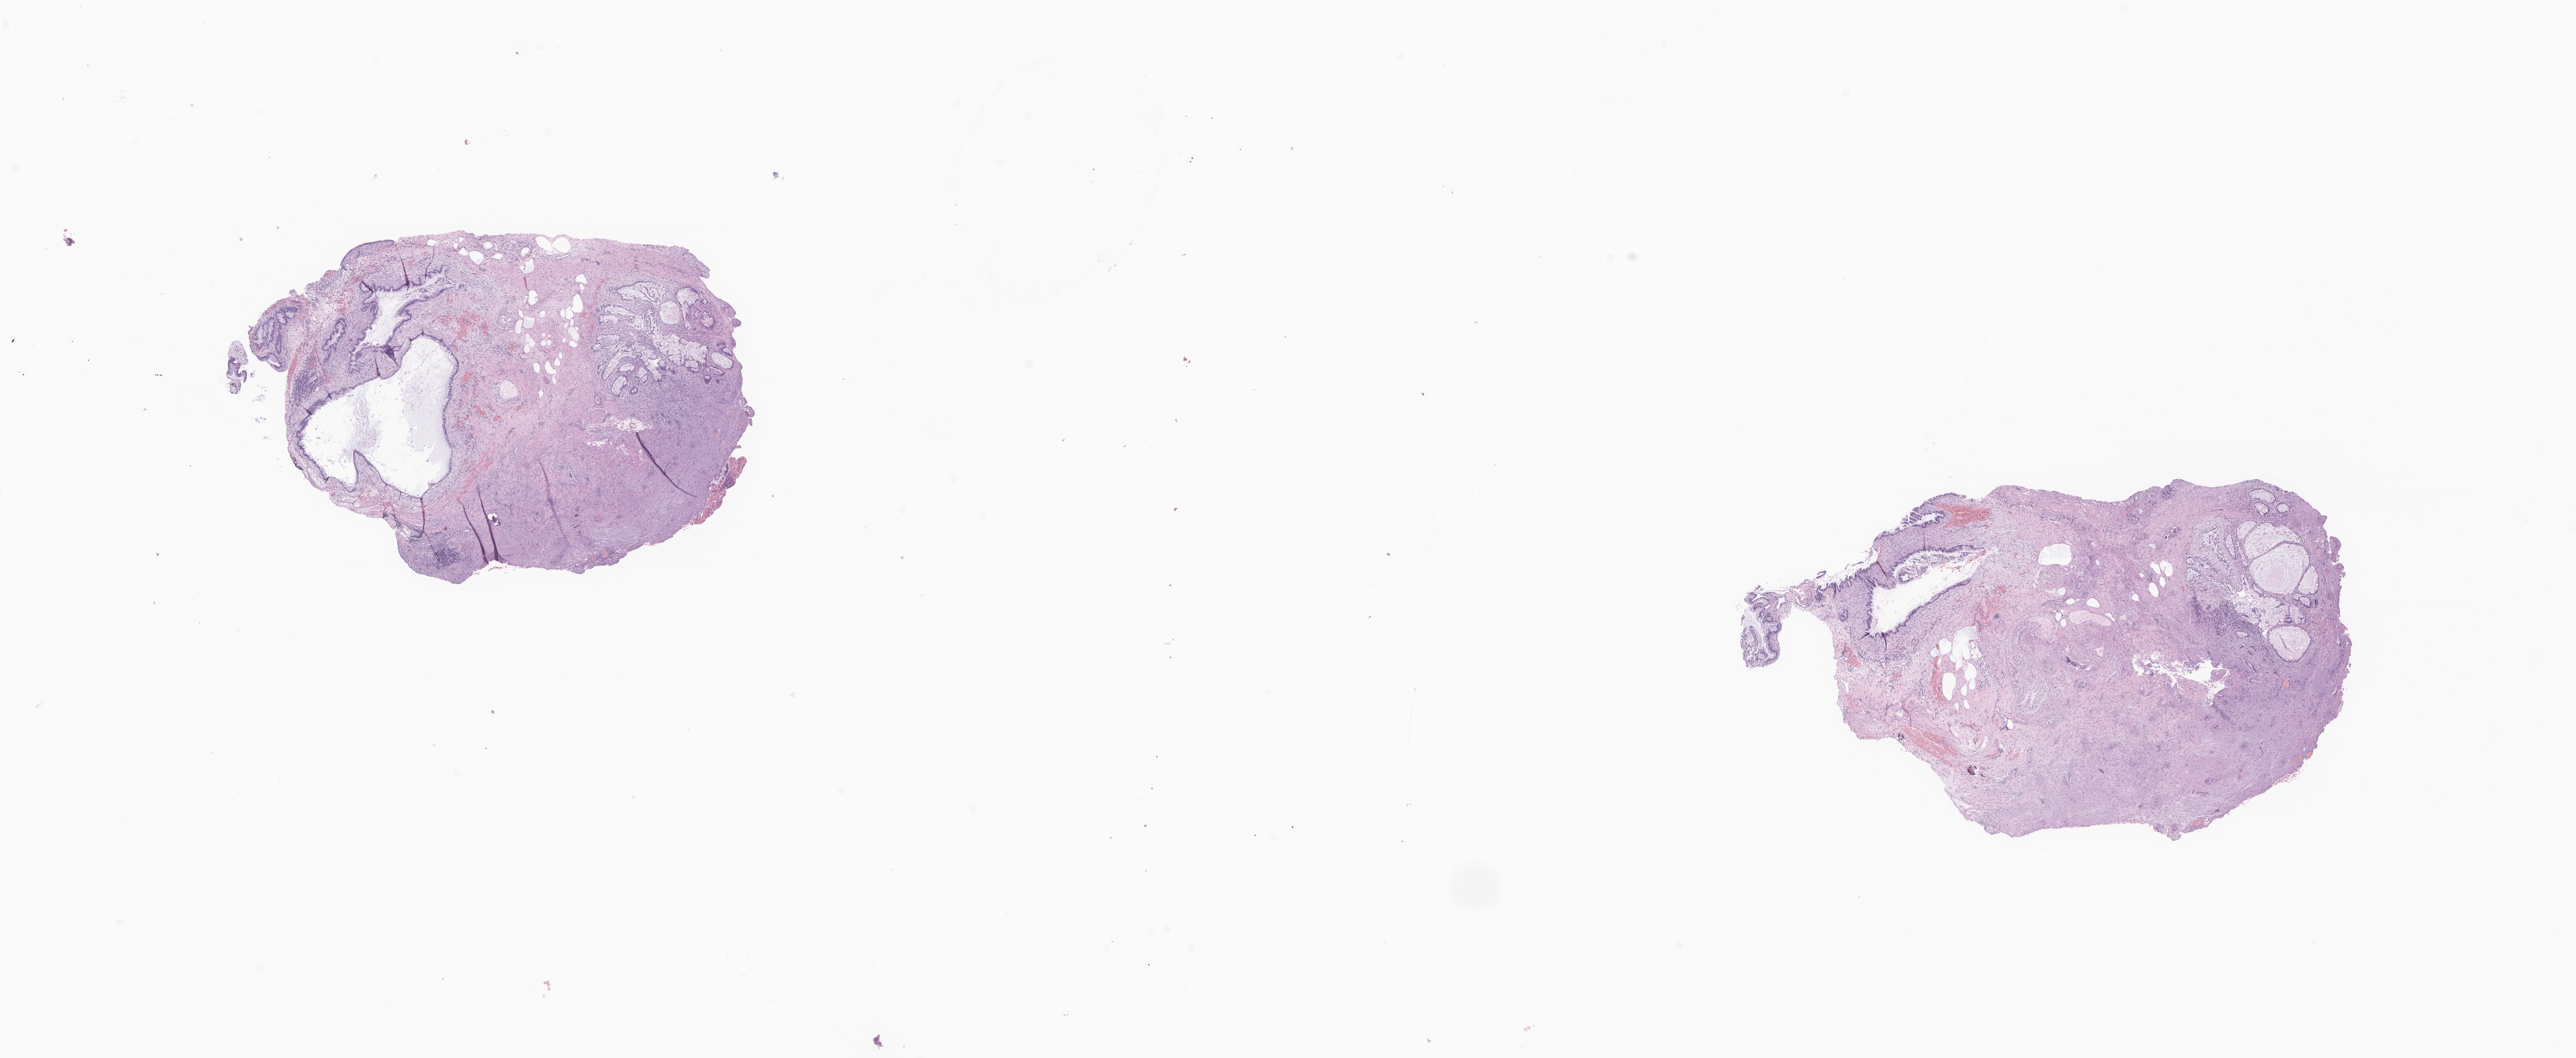
Digitized H&E-stained section of tumor tissue from the cerebral ventricle — a low-resolution overview of the entire scanned area, about 22.2 x 9.1 mm. Formalin-fixed, paraffin-embedded (FFPE) tissue. Male patient, age 138 months (11 years 6 months).
- recorded diagnosis: Teratoma, NOS